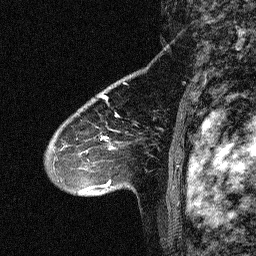
Breast MRI (dynamic contrast-enhanced), one sagittal slice; slice 45 of 64 in the series (ordered by position); dynamic contrast-enhanced study with each time point stored as its own series, time point 2 of 3 at this slice position (early post-contrast, ordered by acquisition time); 1.5 T; TE 4.5 ms, TR 11 ms; 256 × 256 image matrix, field of view 200 × 200 mm. Female patient, age 46 years. Case-level facts recorded for this patient, not image findings: setting: breast cancer imaged before/during neoadjuvant chemotherapy; receptor status: HER2-positive.
Outlined on this slice (semi-automatic segmentation, software-assisted and operator-edited):
- analysis volume of interest (the breast-tissue region the enhancement analysis was run in; not a lesion): bounding box (x1, y1, x2, y2) in pixels: (42, 80, 150, 180)
- tumour enhancement mask (voxels above the 90 % enhancement threshold inside the analysis volume of interest): (65, 97, 127, 151)